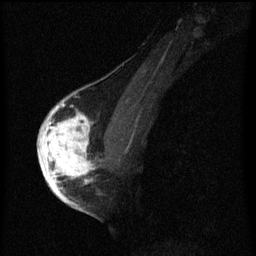
Breast MRI (dynamic contrast-enhanced), one sagittal slice; dynamic contrast-enhanced series, image 2 of 3 at this slice position (ordered by acquisition); 1.5 T; TE 4.2 ms, TR 8 ms; 256 × 256 image matrix, field of view 180 × 180 mm. Female patient, age 56 years.
Structures marked on this image (semi-automatically segmented with operator editing):
- analysis volume of interest (the breast-tissue region the enhancement analysis was run in; not a lesion): bounding box (x1, y1, x2, y2) in pixels: (42, 110, 99, 193)
- tumour enhancement mask (voxels above the 70 % enhancement threshold inside the analysis volume of interest): (42, 110, 95, 193)